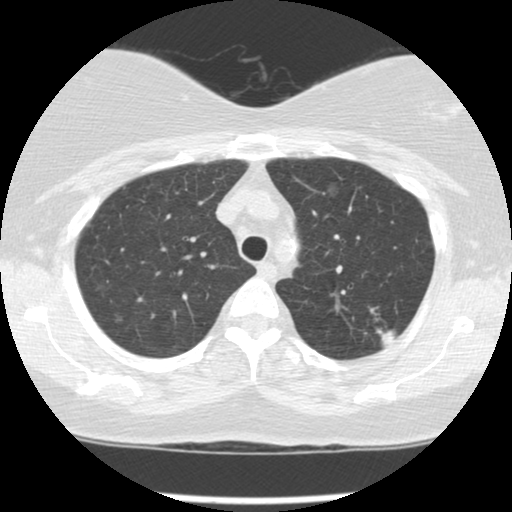
Low-dose screening chest CT, axial slice, third screening round (two years after baseline), lung window (W 1500 / L -600 HU), 2.5 mm slice thickness. Female, age 56 years at enrolment. Current smoker at enrolment.
Lesion marked by an expert reader, box from (x=340, y=304) to (x=415, y=364) px. The screening reader recorded 4 non-calcified nodules or masses ≥4 mm on this exam (left upper lobe, left upper lobe, left upper lobe, right upper lobe); which of them this box marks is not recorded. Later outcome: lung cancer diagnosed 49 days after this screen — adenocarcinoma, NOS, left upper lobe, moderately differentiated (G2), stage IA (AJCC 6th edition), 10 mm at pathology.